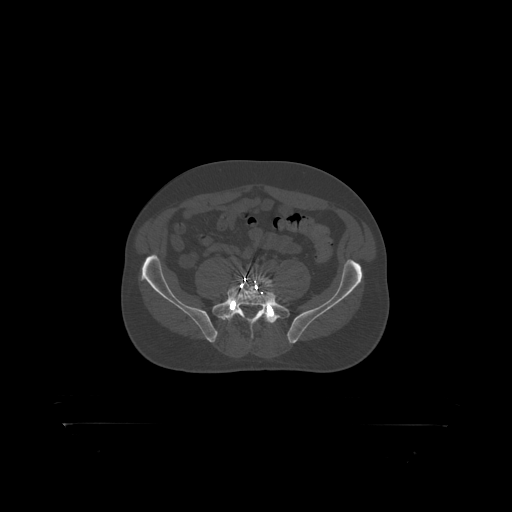
CT including the spine, one axial slice; position 189 of 399 along the scan axis; reconstruction kernel STANDARD; 120 kVp; bone window (W 1800 / L 400 HU); 512 × 512 image matrix, field of view 650 × 650 mm. Male patient, age 46 years. From the clinical record (not read from this slice): primary cancer: skin.
Annotated regions visible in this slice (semi-automatic segmentation, software-assisted and operator-edited):
- L5 vertebra: box from (x=255, y=276) to (x=274, y=292) px